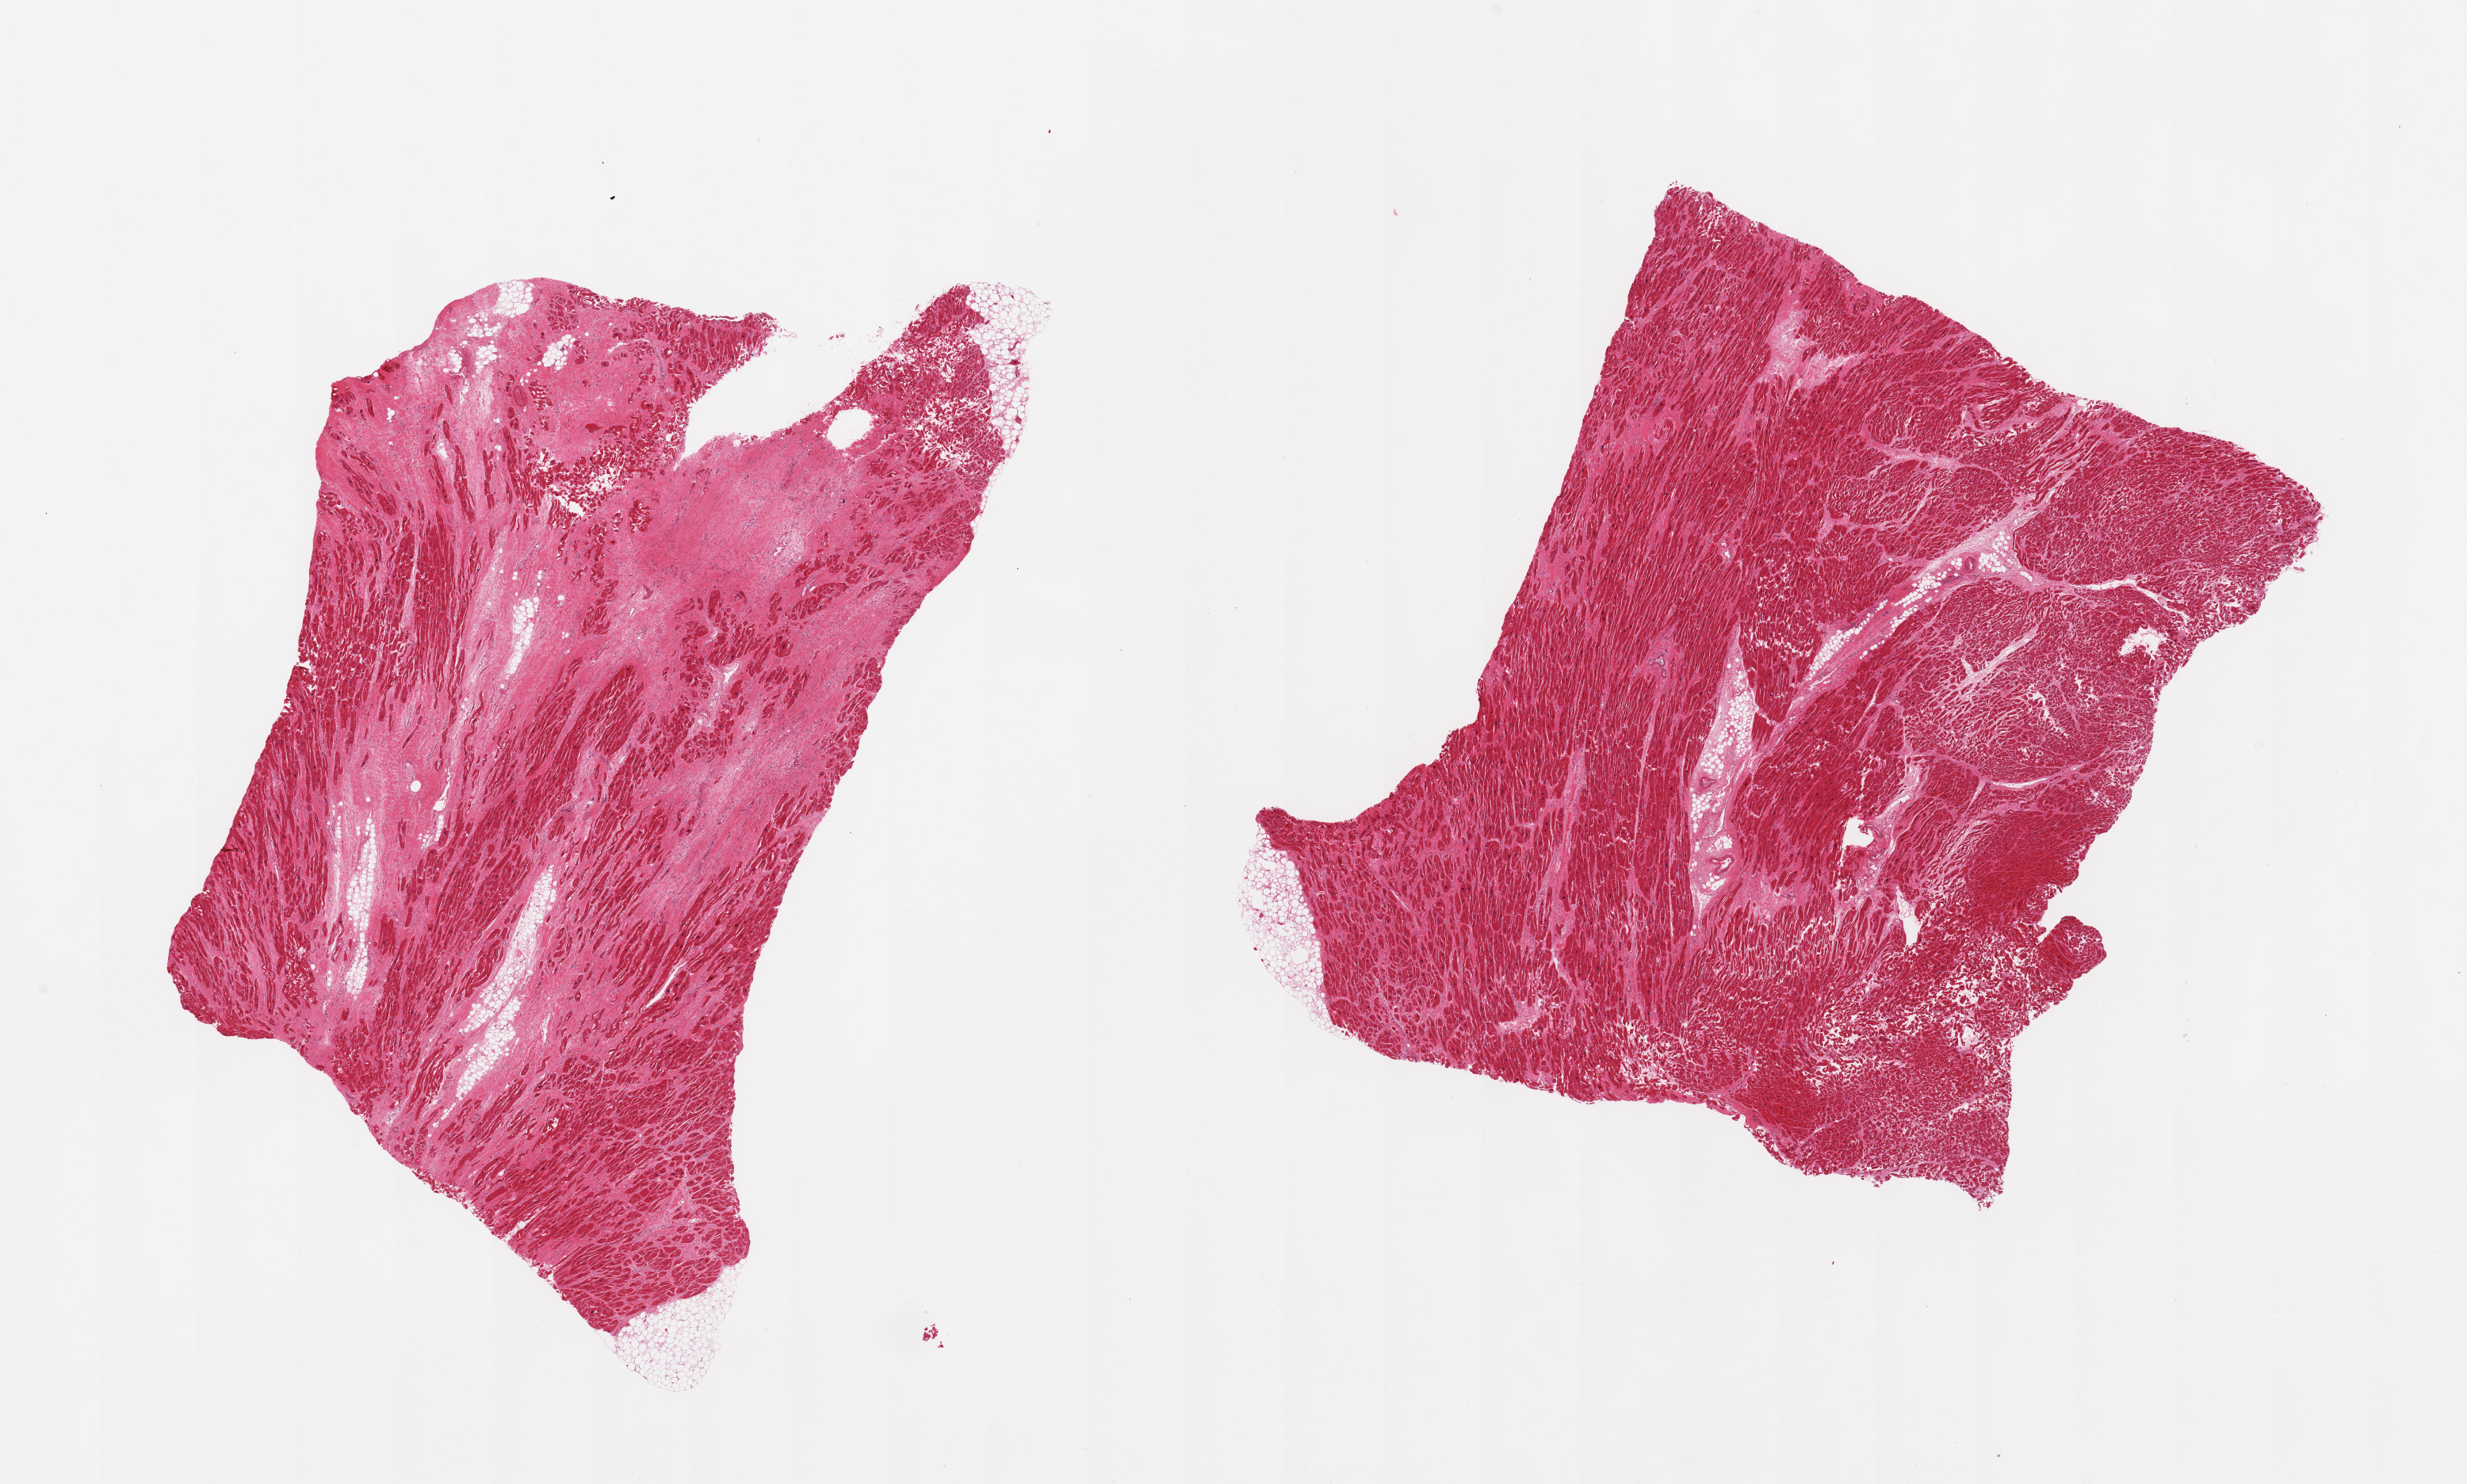
Digitized H&E-stained section, brightfield — low-resolution overview of the scanned area, about 24.6 x 14.8 mm; PAXgene-fixed paraffin-embedded (PFPE) section; section of heart (target tissue); donor tissue sample. Male donor.
Pathologist's review note for this sample: 2 pieces; 50% fibrous scar in 1 piece, 10% in other; consistent with old infarcts.